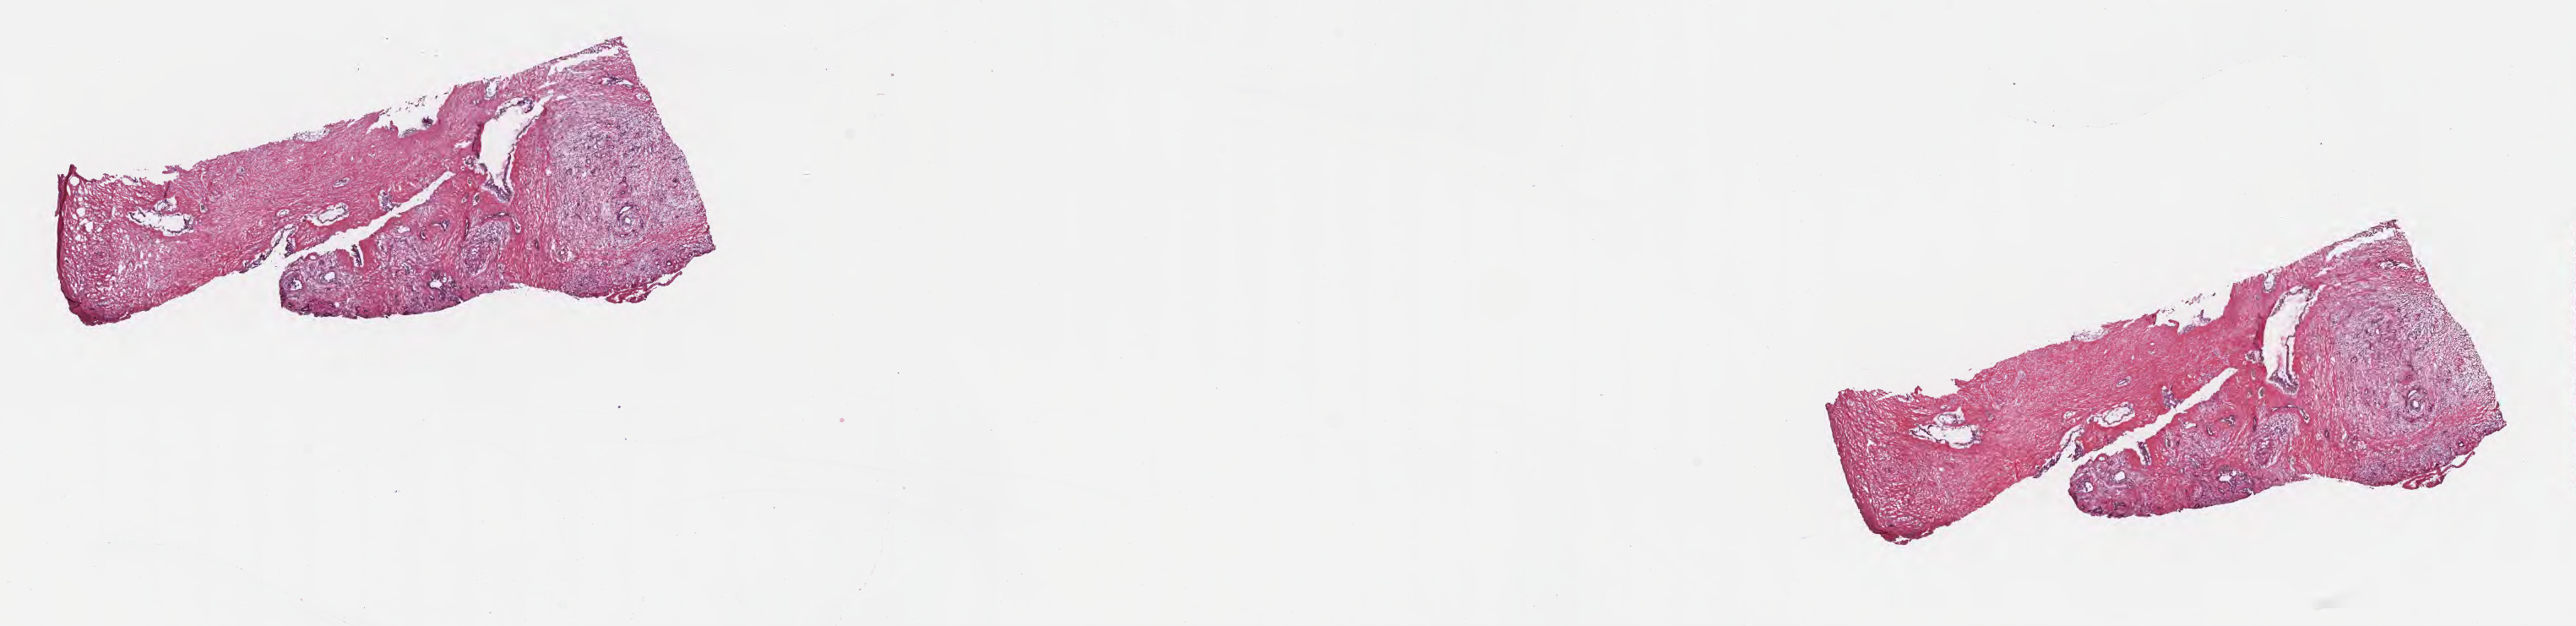
H&E whole-slide image, low-resolution overview of the scanned area, about 24.7 x 6.0 mm; cryosection; specimen: primary tumor; anatomic site: head of pancreas. Female patient; age at initial diagnosis 70 years. Tumor grade: G2 (moderately differentiated). Pathologist review of this section (percent, as recorded): tumor cells 40%, tumor nuclei 50%, stromal cells 60%, necrosis 0%, normal cells 0%. Infiltration values recorded for this section: lymphocyte infiltration 0%, monocyte infiltration 0%, neutrophil infiltration 0%.
* diagnosis: Infiltrating duct carcinoma, NOS
* section: top of the tissue portion
* AJCC pathologic stage: Stage IIB